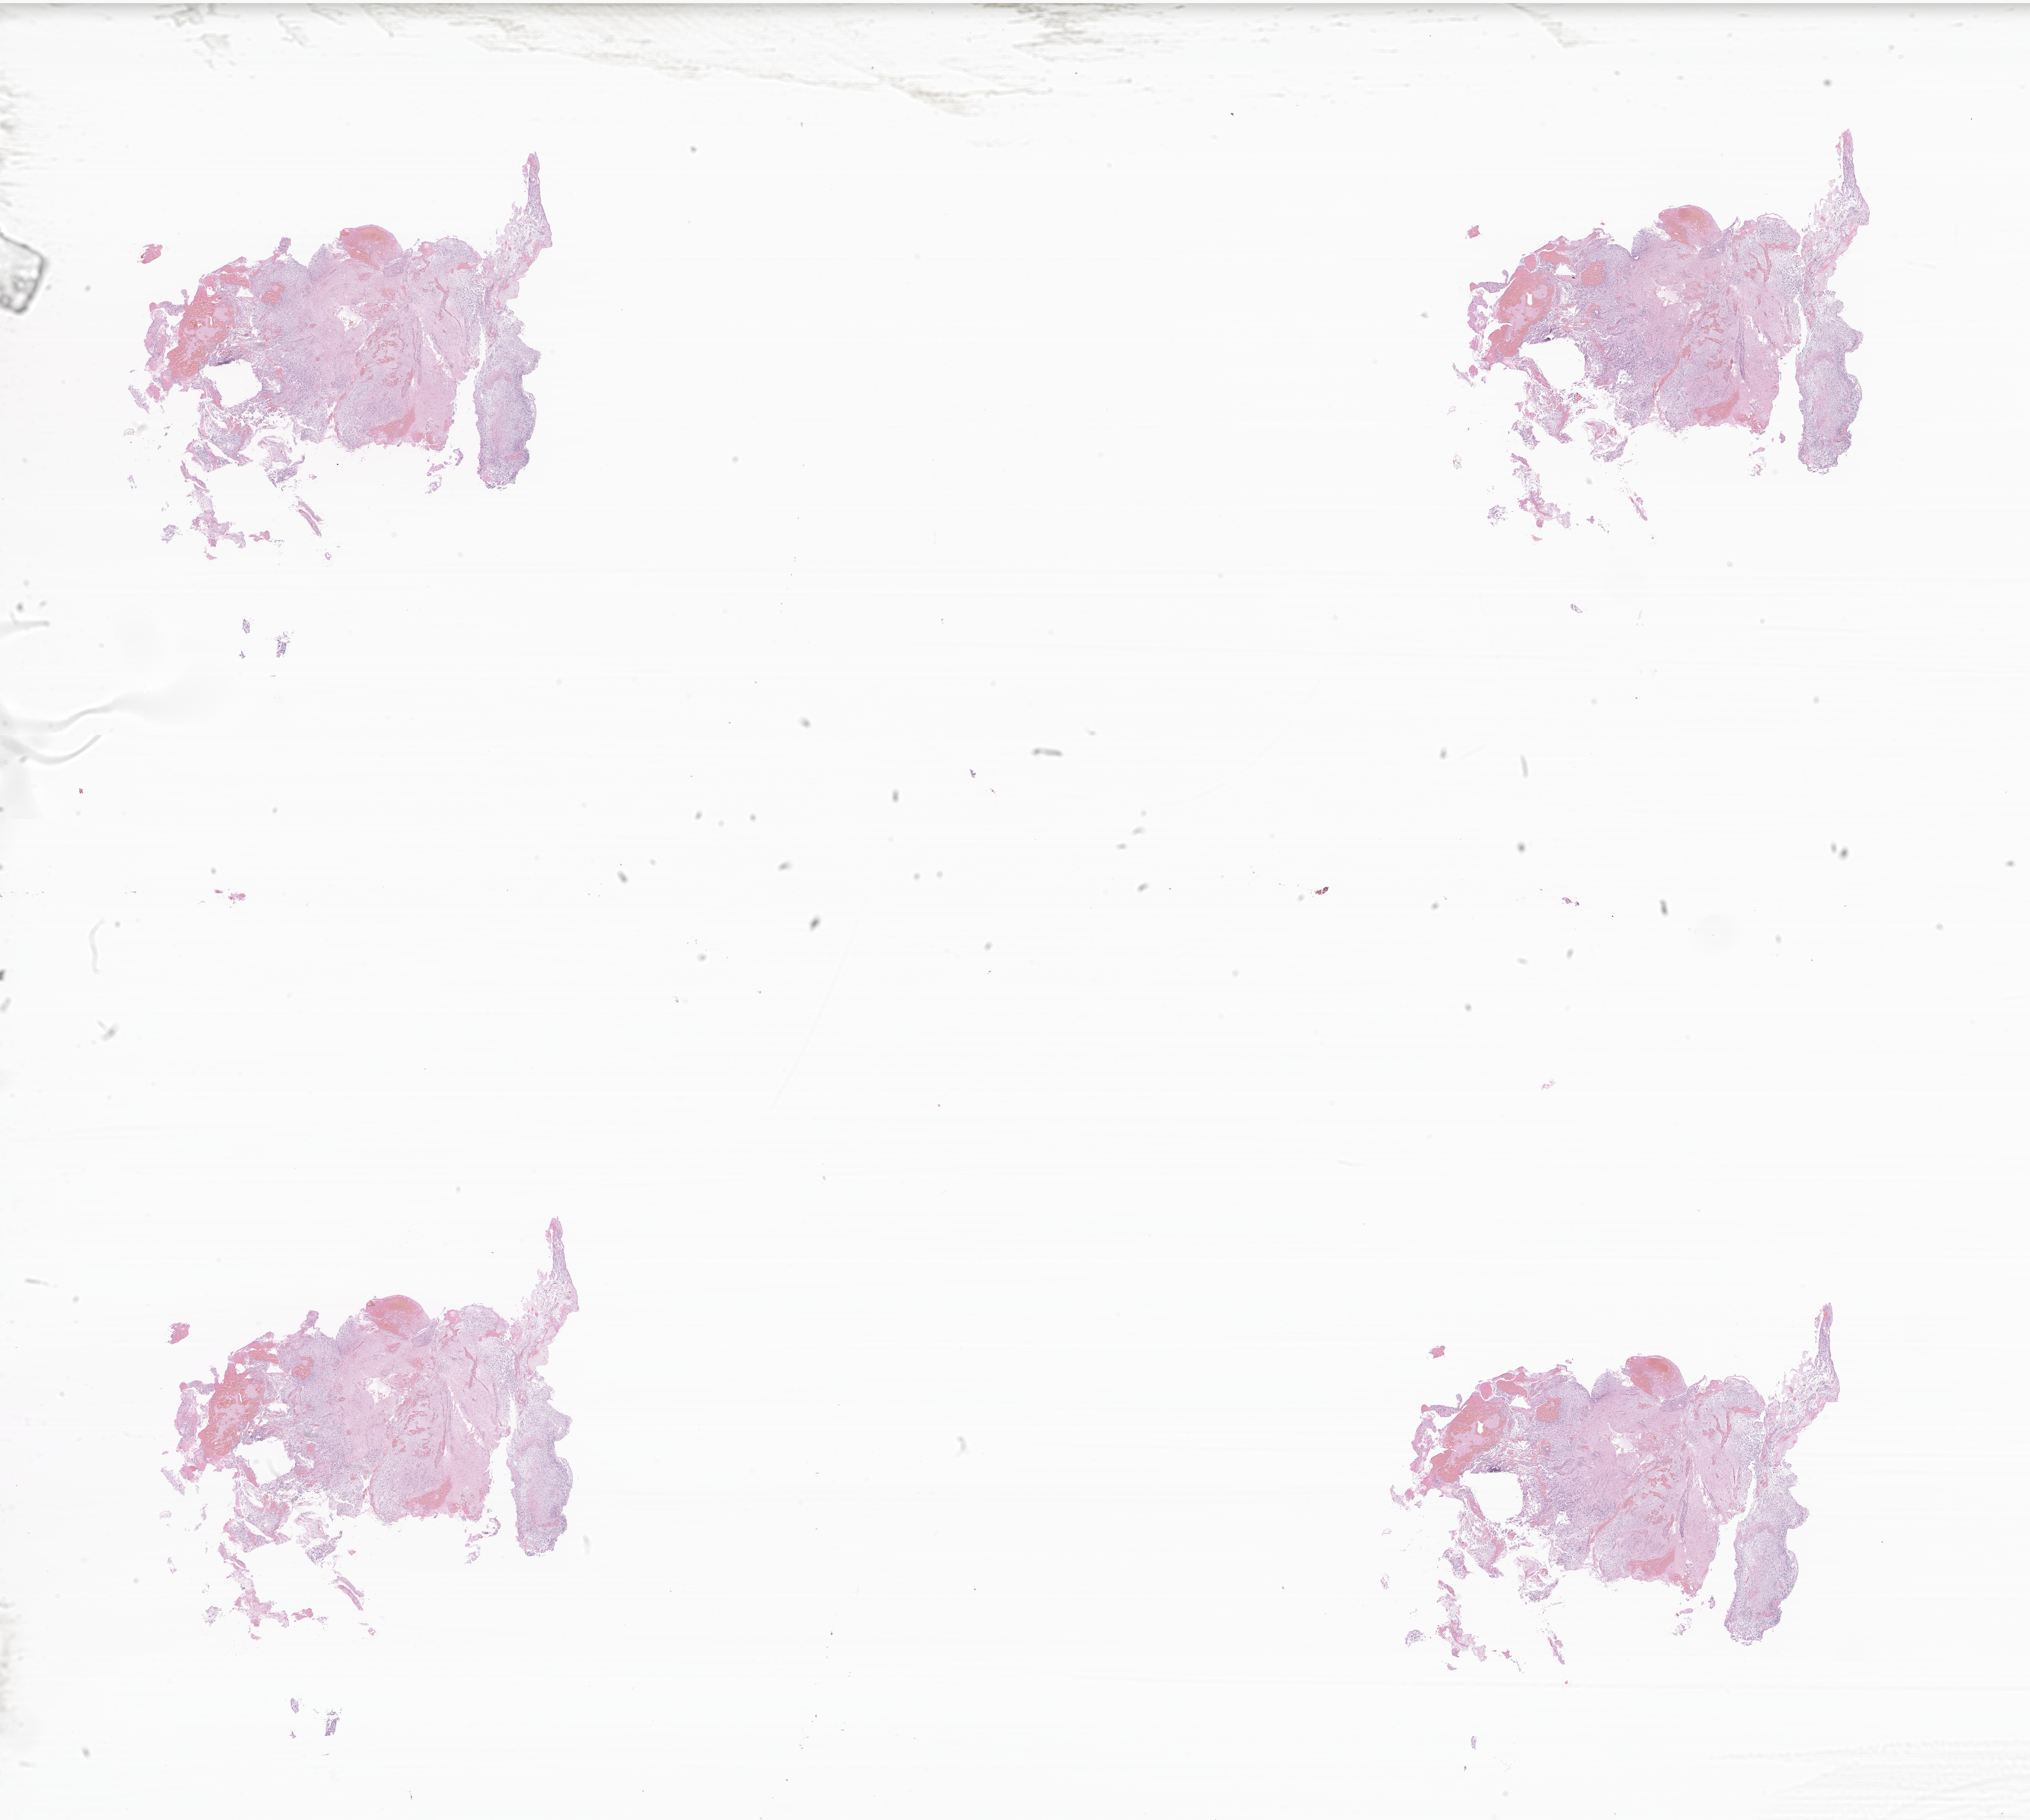
Whole-slide image, haematoxylin and eosin stain of tumor tissue from the spinal cord — shown as a low-resolution overview of the whole scanned area (about 25.7 x 23.0 mm), formalin-fixed paraffin-embedded section. Patient female; age 39 months.
- diagnosis (ICD-O-3 morphology term): Glioma, malignant